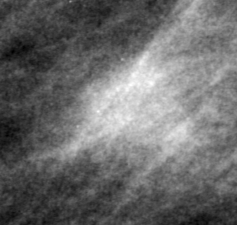
Crop from a digitized film mammogram around one marked abnormality, left breast, MLO view, BI-RADS breast density category 2 (scale 1–4).
Finding: mass, shape irregular, margins ill defined; BI-RADS assessment category 4; pathology result (as recorded, not read from the image): malignant.